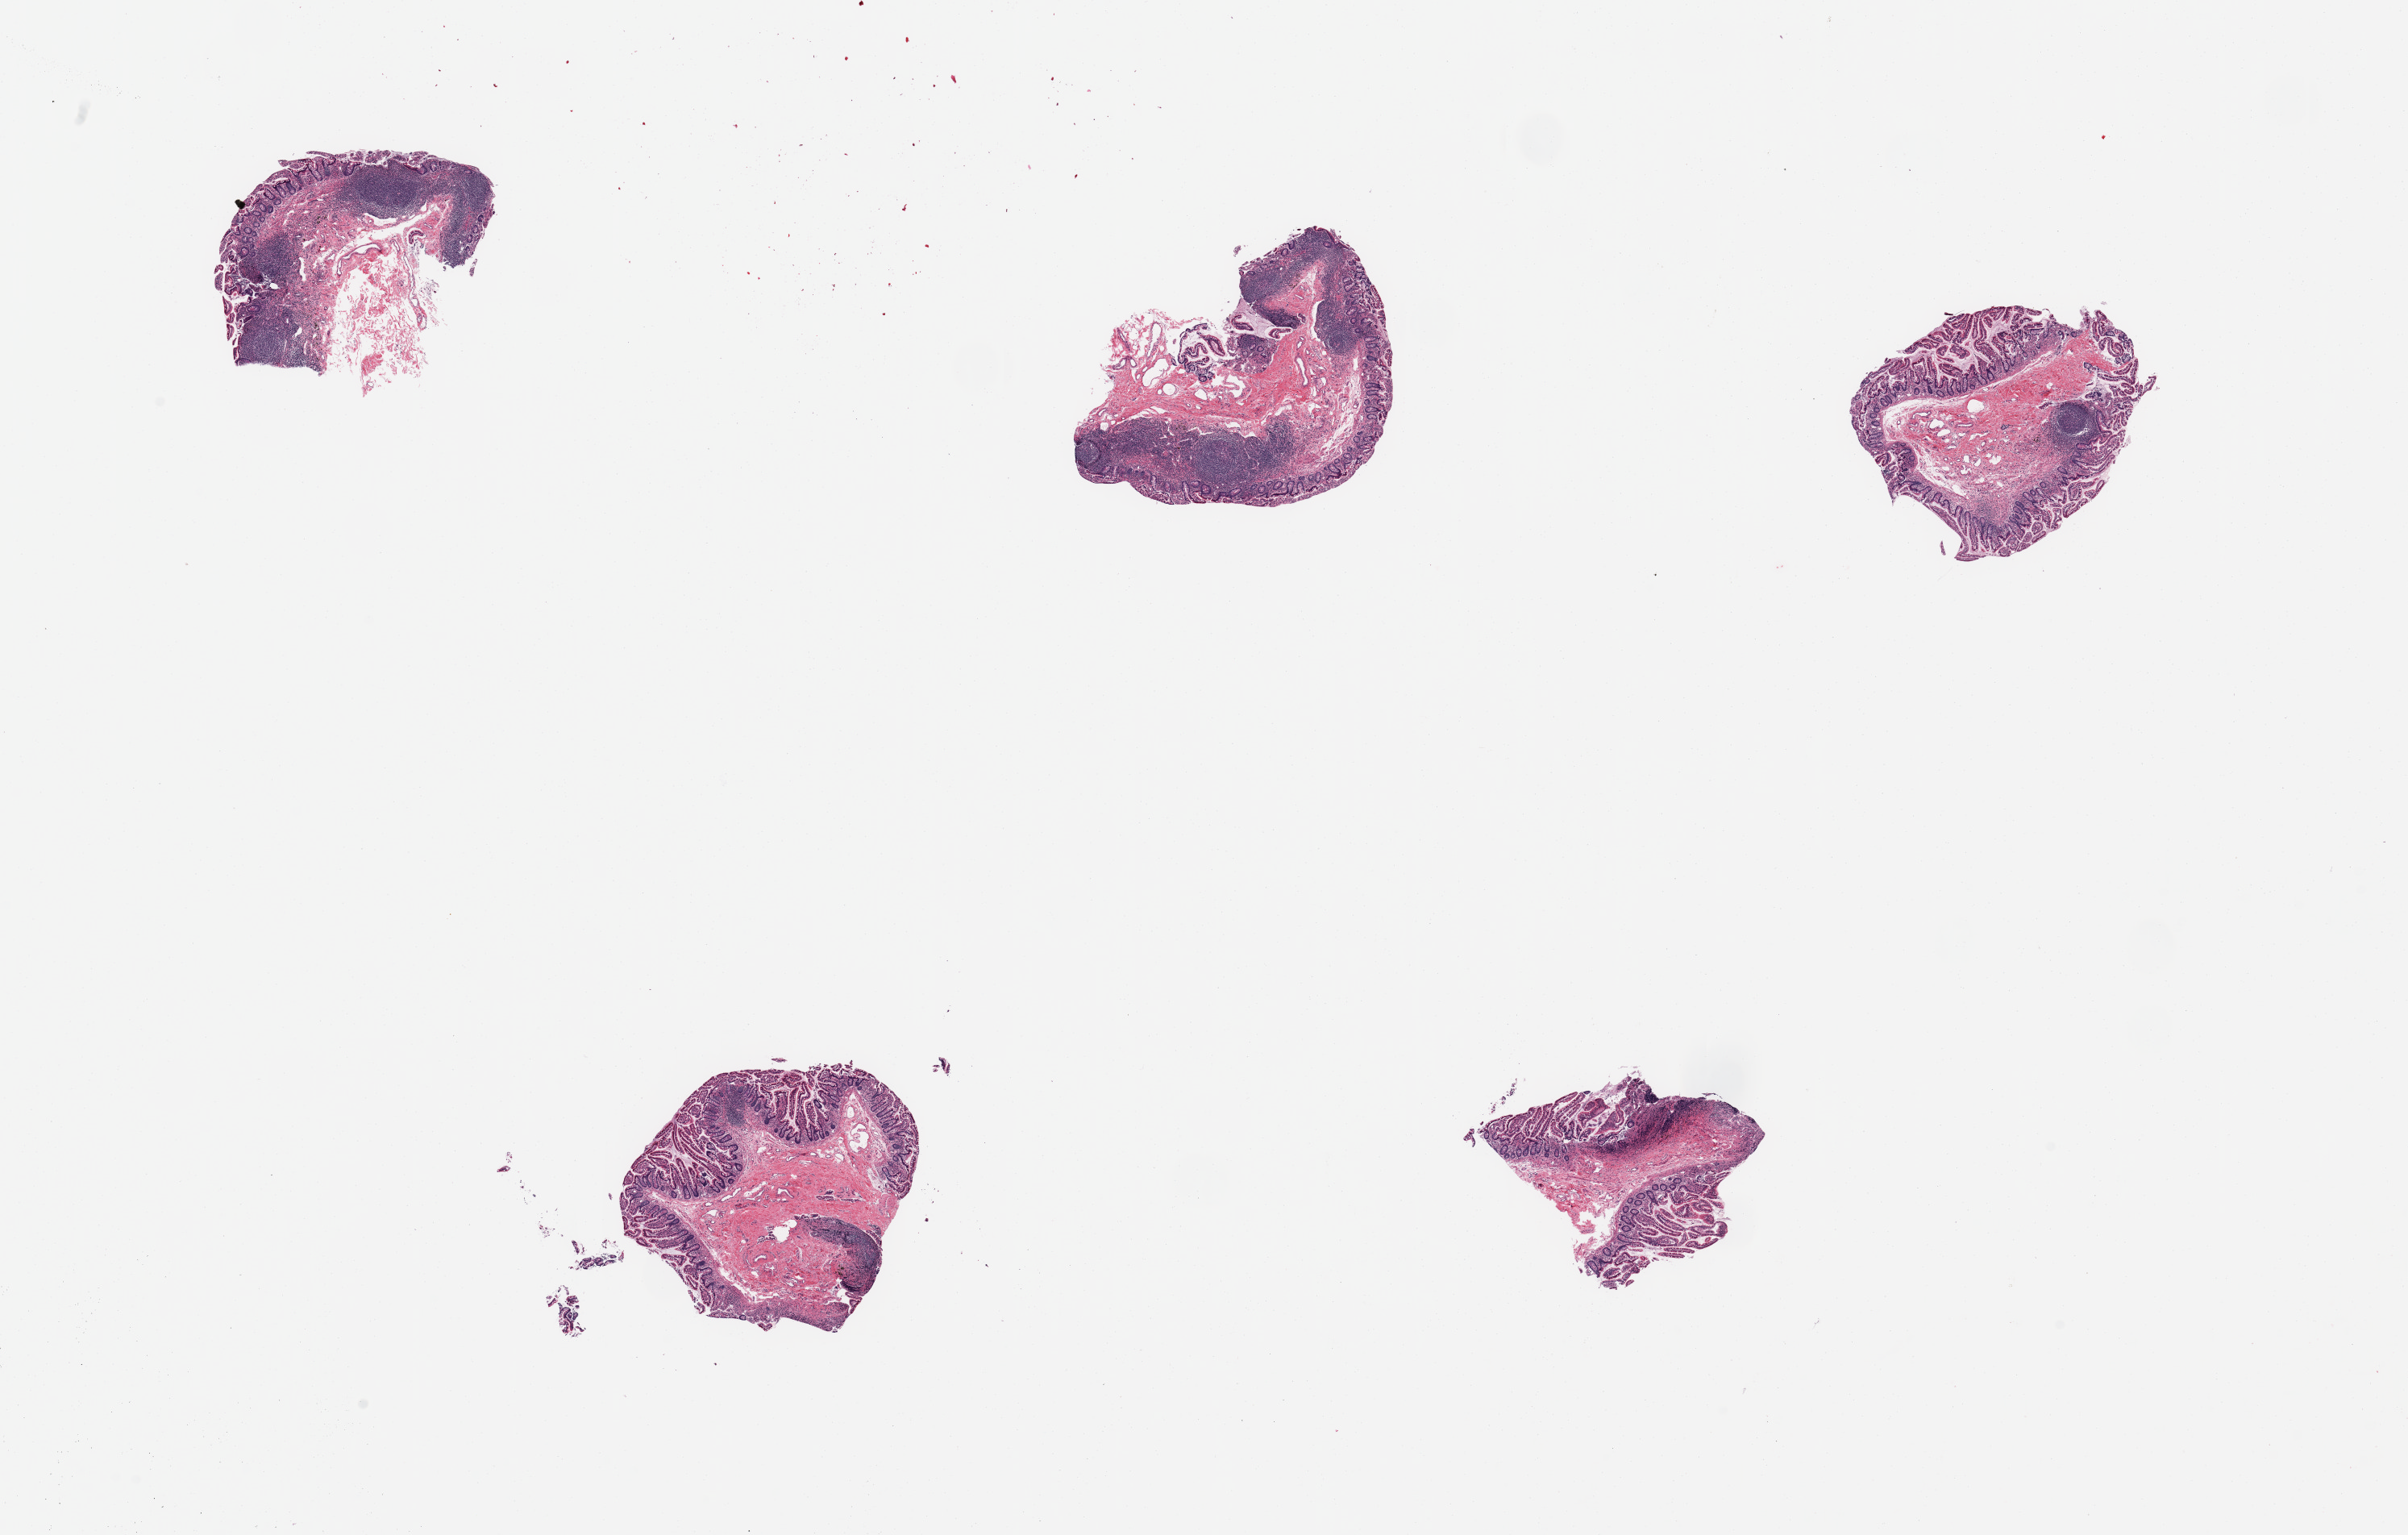
Digitized H&E-stained section, whole scanned area (about 23.6 x 15.1 mm) shown as a low-resolution overview. Donor sex: female.
* specimen: PAXgene-fixed paraffin-embedded (PFPE) section; section of ileum (target tissue); tissue donor sample